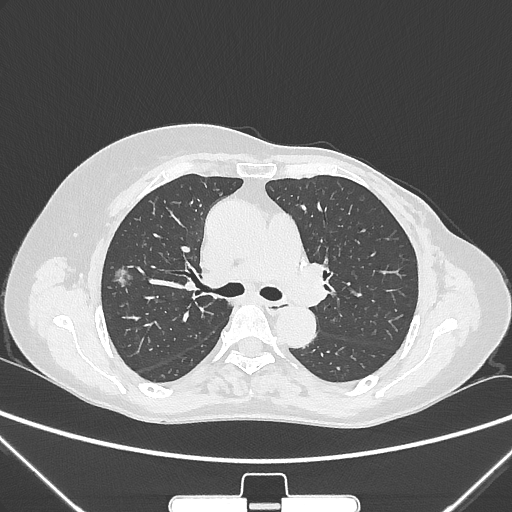
Chest CT, one axial slice. Slice 161 of 265 in the series (ordered by position). Lung window (W 1500 / L -600 HU). 512 × 512 image matrix, field of view 350 × 350 mm. Patient: female, 64 years. Case-level facts recorded for this patient, not image findings: clinical TNM (as recorded): T1c N0 M0; histopathological grade: G1-2.
Annotated regions visible in this slice (rectangle marked by the reading radiologist):
- lung tumour (recorded histology: adenocarcinoma): bounding box (x1, y1, x2, y2) in pixels: (109, 259, 137, 296)